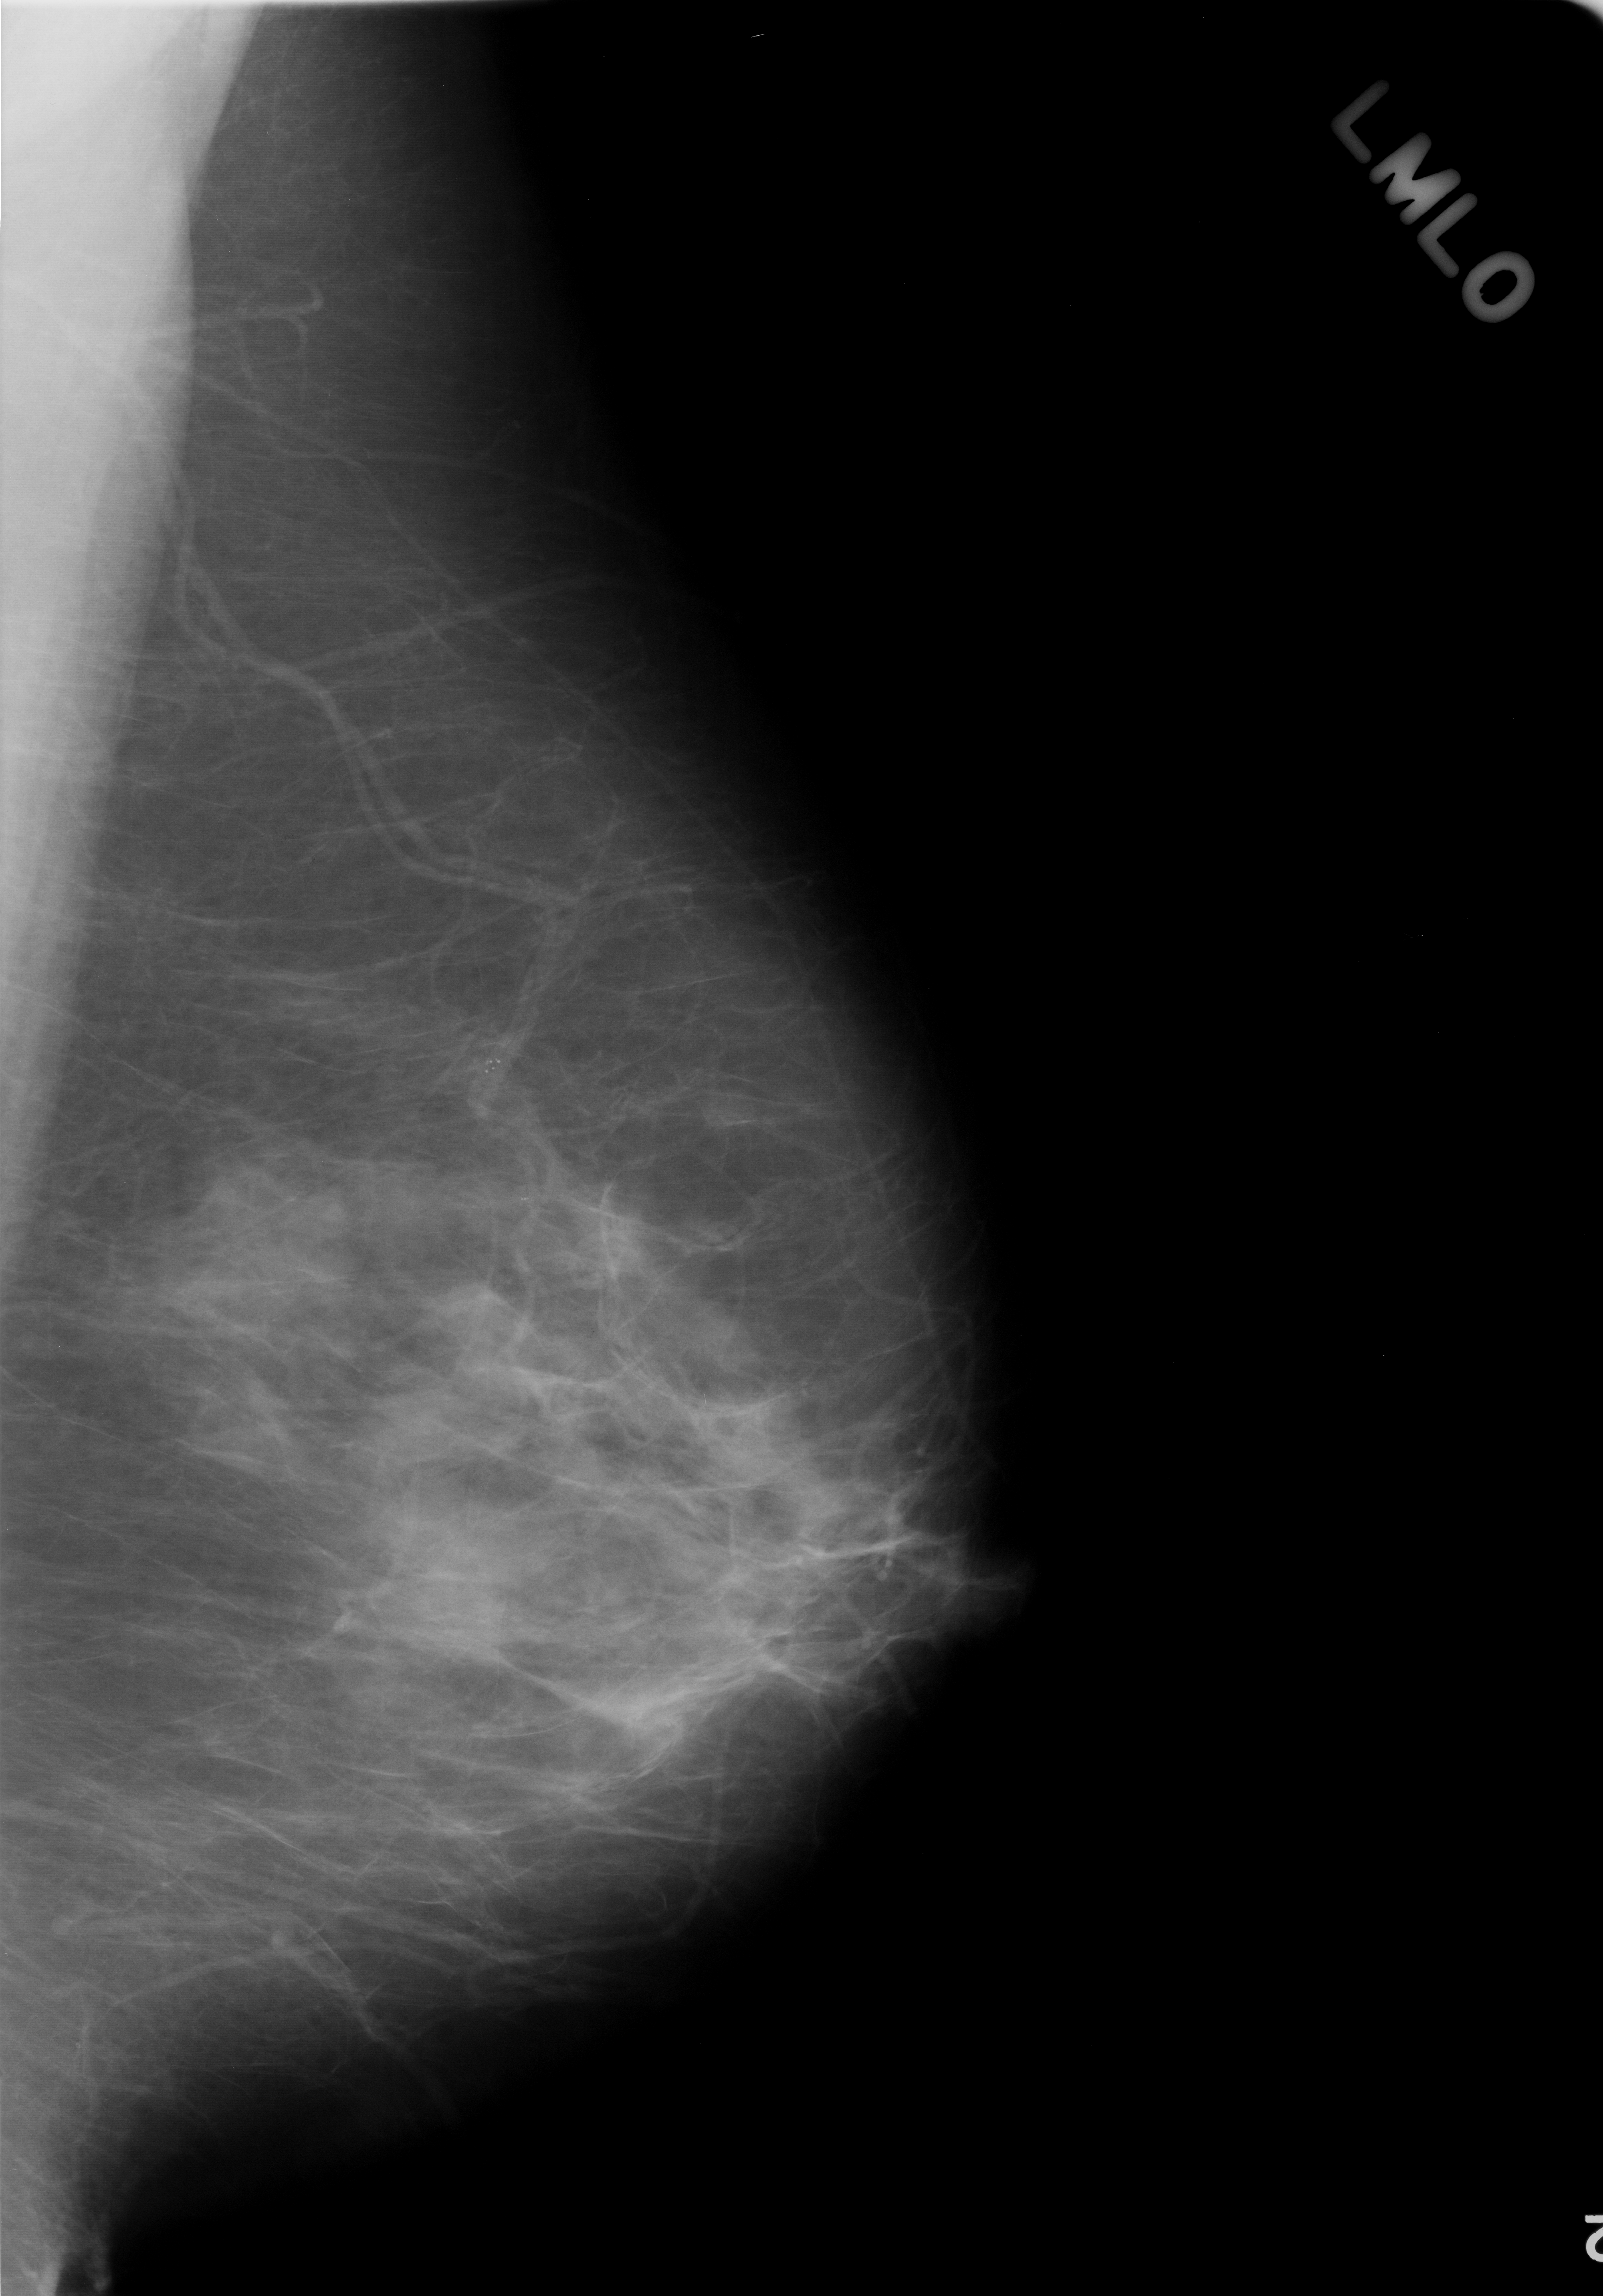
Mammogram (digitized film); left breast; MLO view; BI-RADS breast density category 2 (scale 1–4).
Abnormality record for this image: calcifications, morphology punctate, distribution clustered; BI-RADS assessment category 3; pathology result (as recorded, not read from the image): benign.